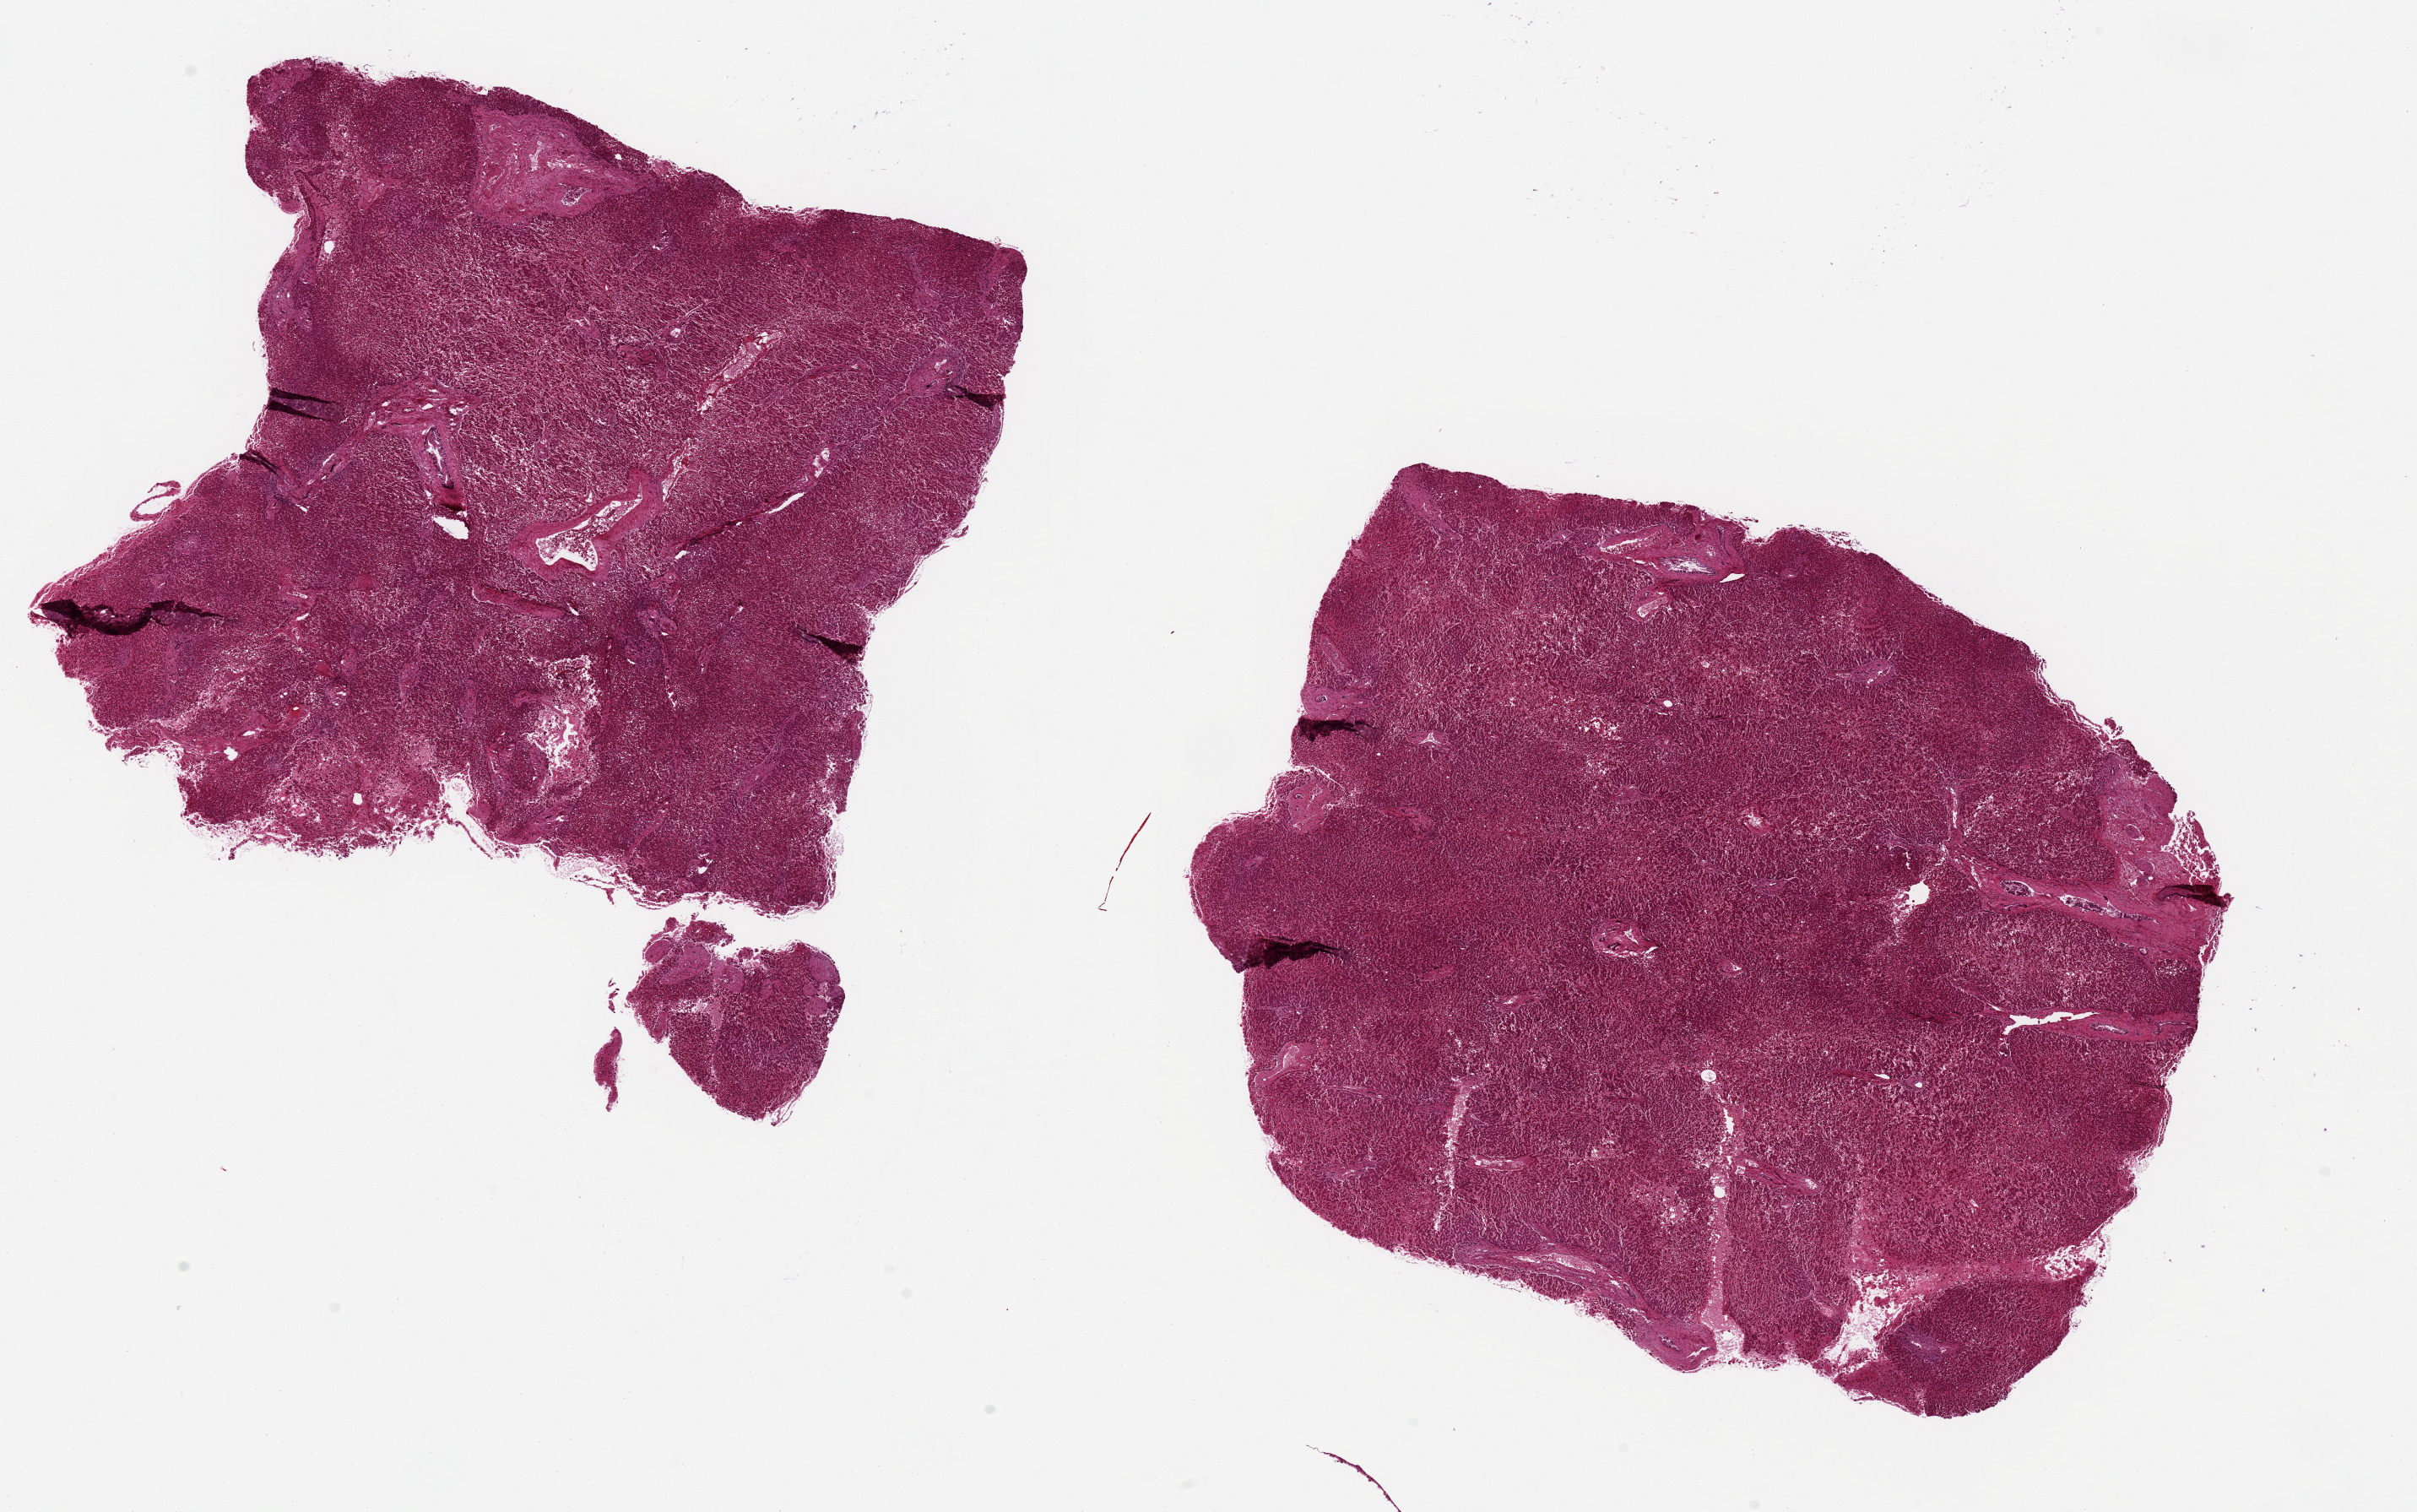
Whole-slide image, hematoxylin and eosin (H&E) stain, brightfield — a low-resolution overview of the entire scanned area, about 22.6 x 14.2 mm (slide scanned at 20x). PAXgene-fixed, paraffin-embedded tissue. Sampled site (target tissue): liver. Tissue donor sample. Female donor.
Reviewer comment on this tissue sample: 2 alquots, ~8x7mm, badly autolyzed.